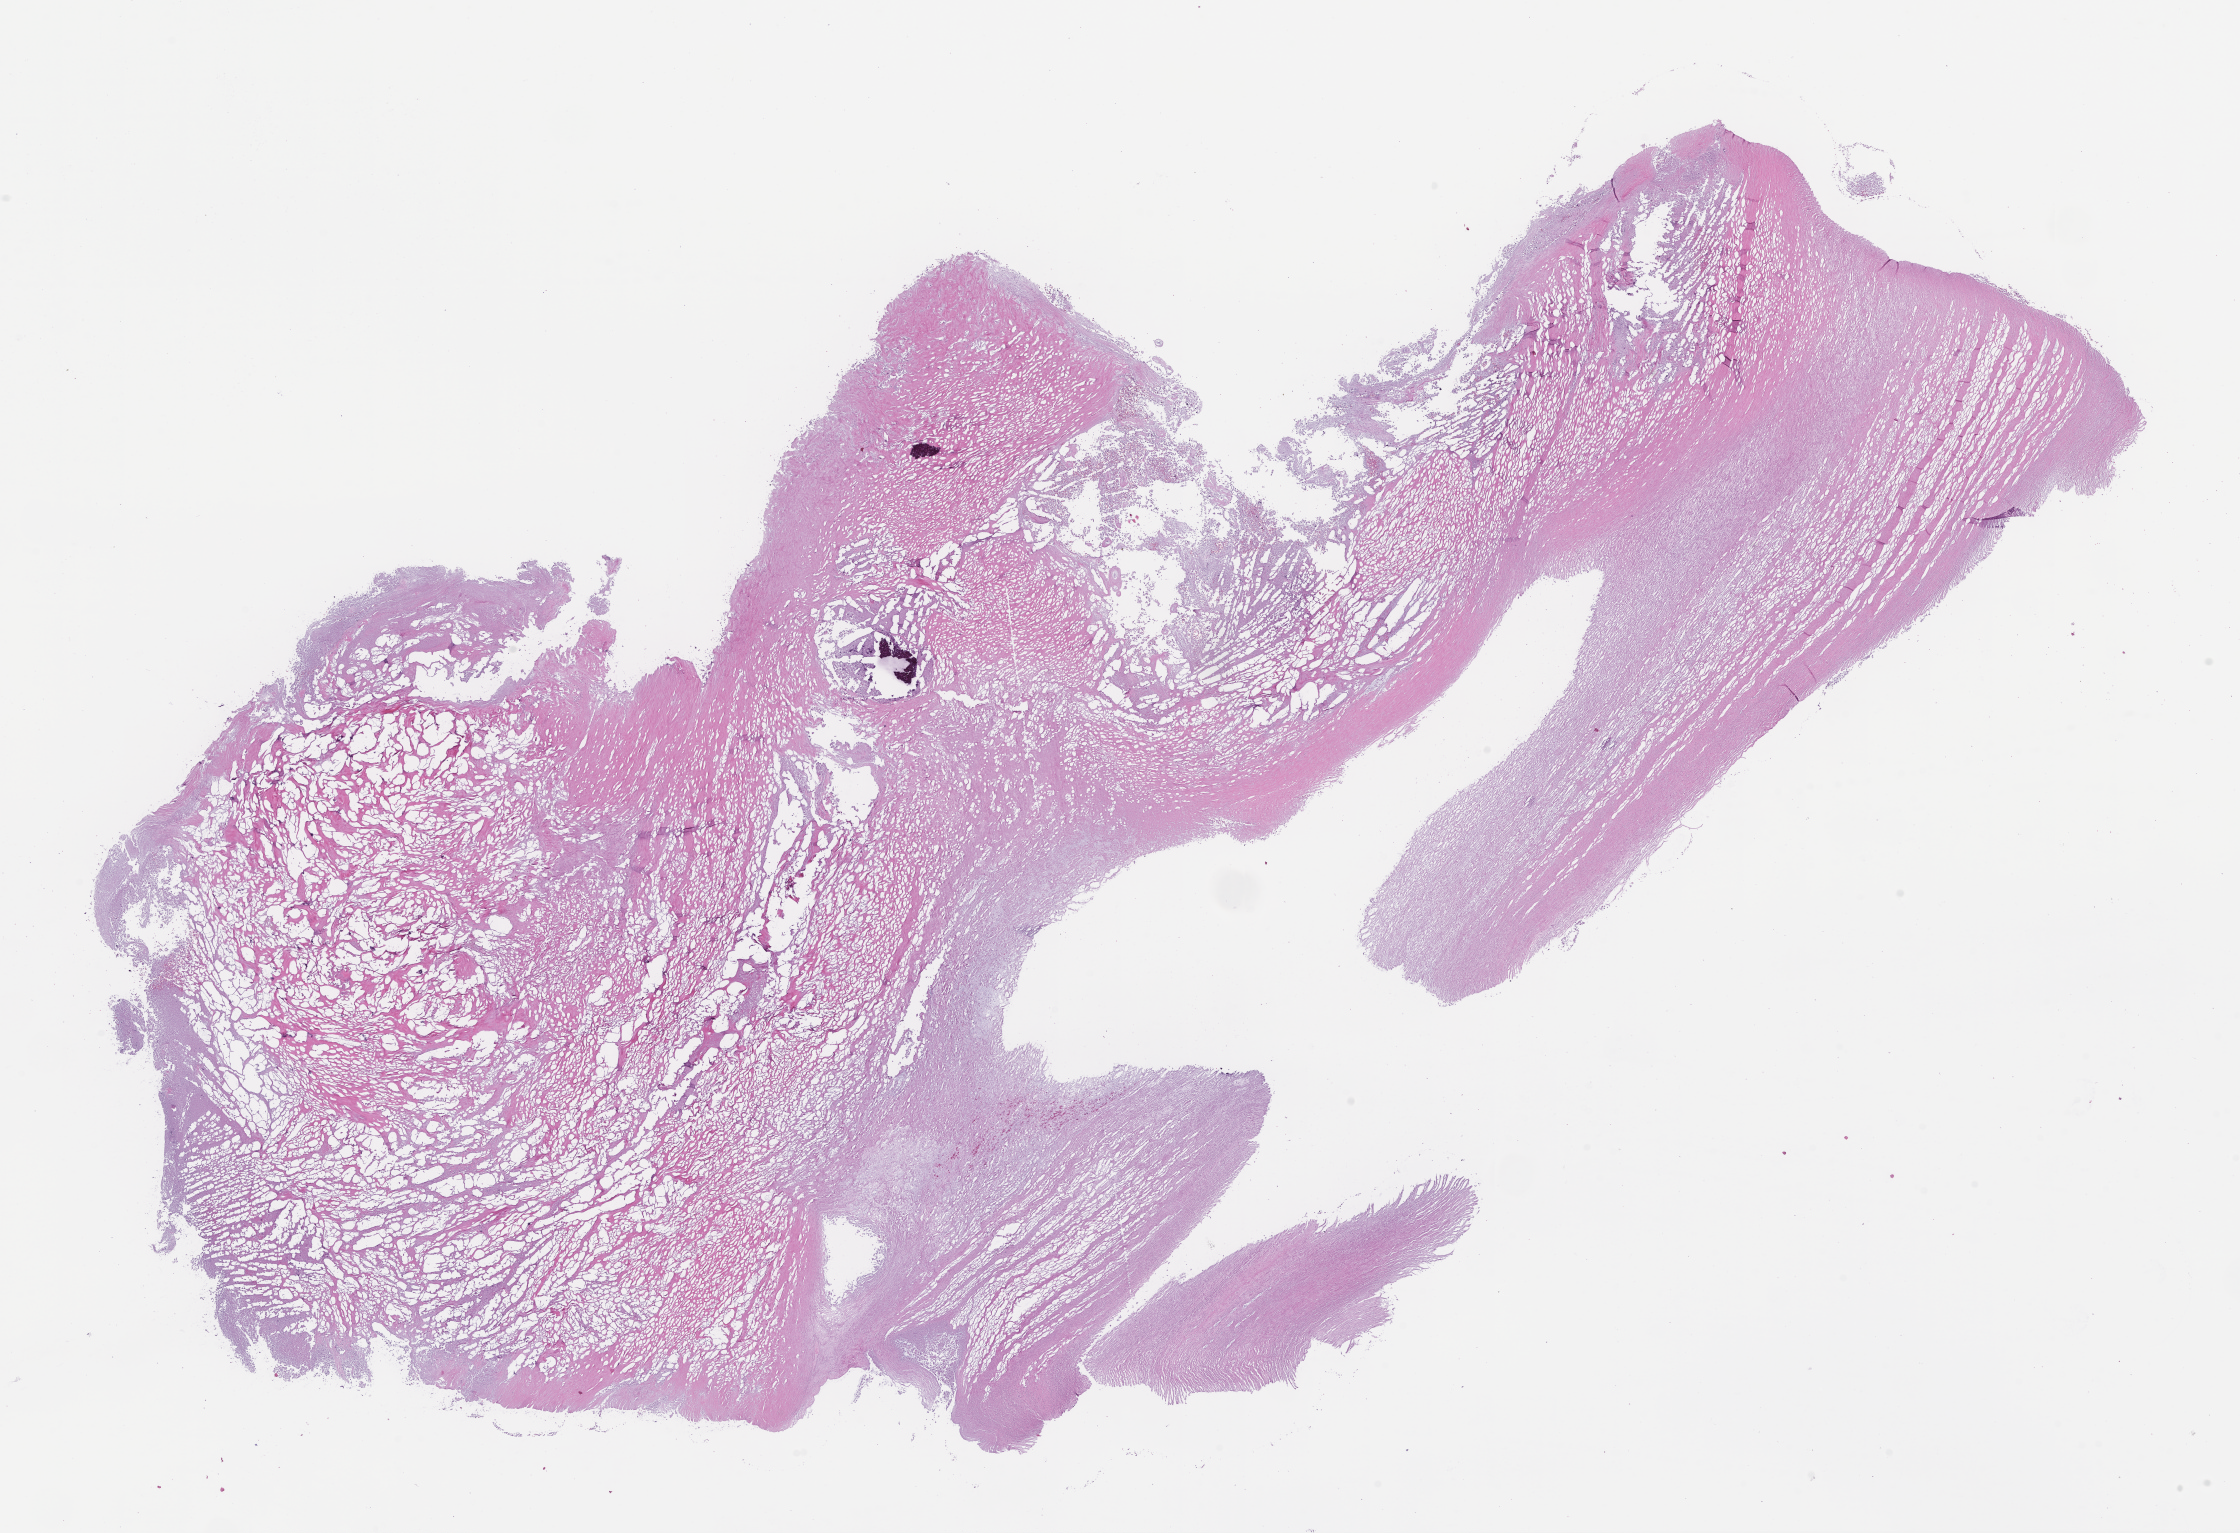
Whole-slide image, haematoxylin and eosin stain — shown as a low-resolution overview of the whole scanned area (about 18.1 x 12.4 mm). Formalin-fixed paraffin-embedded section. Tissue site: ovary. Specimen time point: collected at baseline (before treatment). Patient sex: female.
• this section: primary tumour tissue
• diagnosis: Ovarian Carcinoma